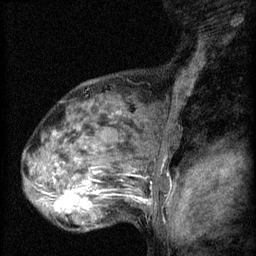
Breast MRI (dynamic contrast-enhanced), one sagittal slice. Slice 44 of 60 in the series (ordered by position). 3 images stored at this slice position (order not interpretable as contrast timing). 1.5 T. TE 4.2 ms, TR 8.2 ms. 2 mm slice thickness. 256 × 256 image matrix, field of view 180 × 180 mm. Female patient, age 48 years.
Outlined on this slice (semi-automatically segmented with operator editing):
- analysis volume of interest (the breast-tissue region the enhancement analysis was run in; not a lesion): bounding box [x1, y1, x2, y2] px = [48, 160, 125, 217]
- tumour enhancement mask (voxels above the 70 % enhancement threshold inside the analysis volume of interest): [54, 178, 92, 213]